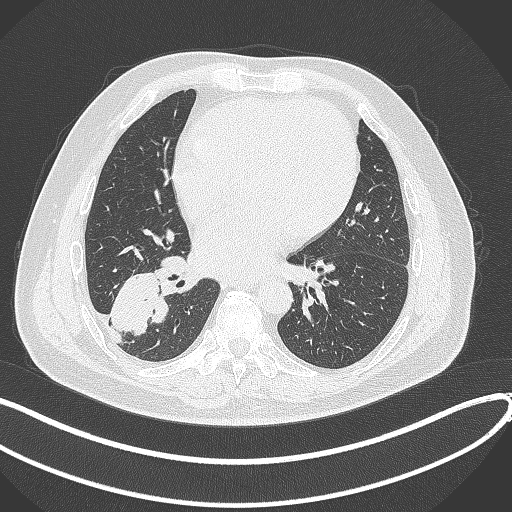
Chest CT, one axial slice; slice 154 of 360 in the series (ordered by position); lung window (W 1500 / L -600 HU); 512 × 512 image matrix, field of view 400 × 400 mm. Patient: male, 59 years.
Outlined on this slice (bounding box drawn by a radiologist):
- lung tumour (recorded histology: adenocarcinoma): bounding box (x1, y1, x2, y2) in pixels: (106, 263, 172, 339)